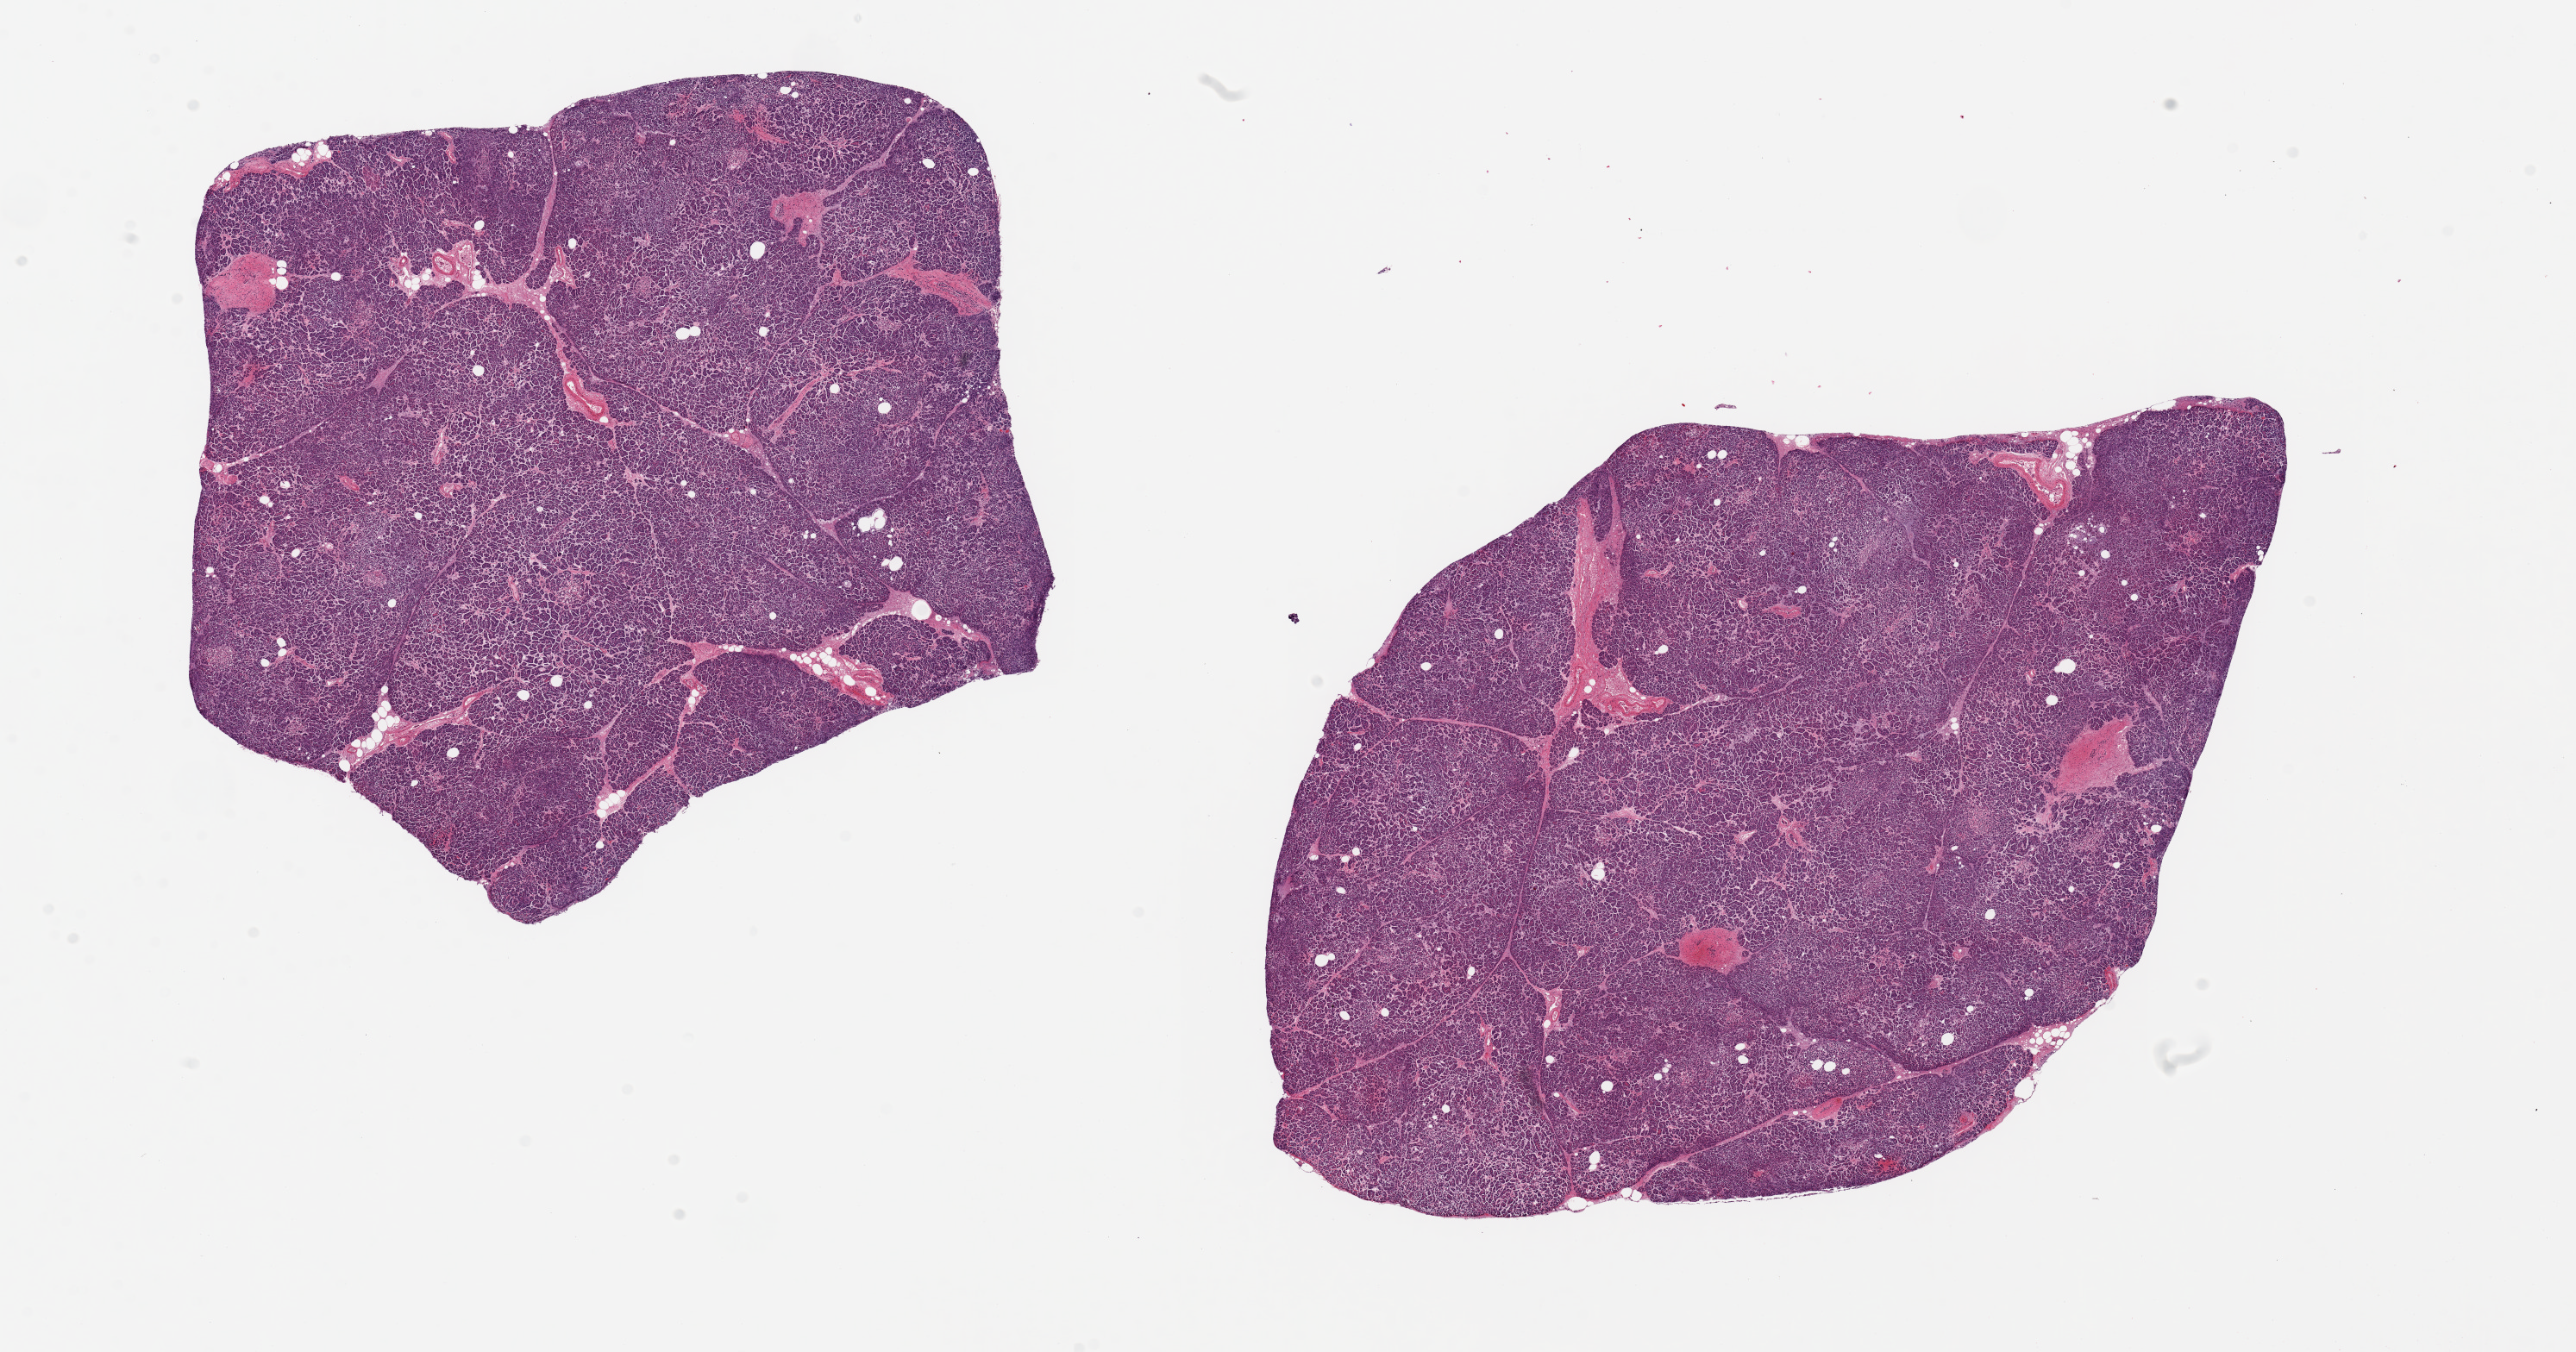
Digitized H&E-stained section, brightfield — low-resolution overview of the scanned area, about 23.6 x 12.4 mm (acquisition: 20x scan), PAXgene-fixed paraffin-embedded (PFPE) section, sampled site (target tissue): pancreas, tissue donor sample. Donor: male.
Pathologist's review note for this sample: 2 pieces, 9x9 & 9x7mm; islets not well visualized, minimal fat.